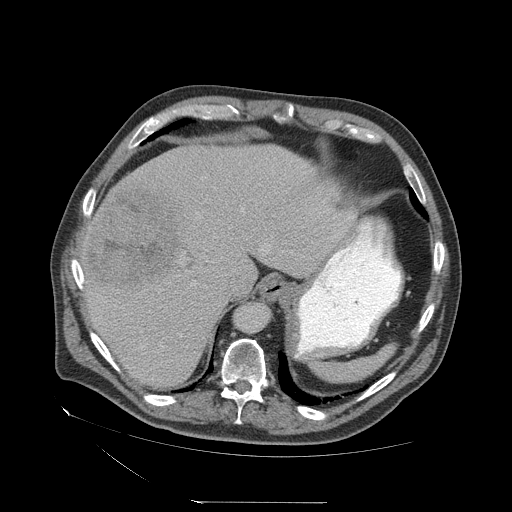
Contrast-enhanced abdominal CT (liver protocol), one axial slice. Position 51 of 83 along the scan axis. Soft-tissue window (W 400 / L 40 HU). 2.5 mm slice thickness. 512 × 512 image matrix, field of view 460 × 460 mm. Case-level facts recorded for this patient, not image findings: diagnosis: hepatocellular carcinoma (patient treated with transarterial chemoembolisation; whether this scan precedes or follows treatment is not stated here); TNM stage (as recorded): Stage-I; Child-Pugh class: A.
Structures marked on this image (semi-automatic segmentation, software-assisted and operator-edited):
- liver parenchyma outside the tumour (the mass and vessels are separate outlines, so this box may not span the whole liver): bounding box <82,144,356,388> (left, top, right, bottom; pixels)
- mass: <86,185,181,294>
- liver vessels: <82,280,84,282>